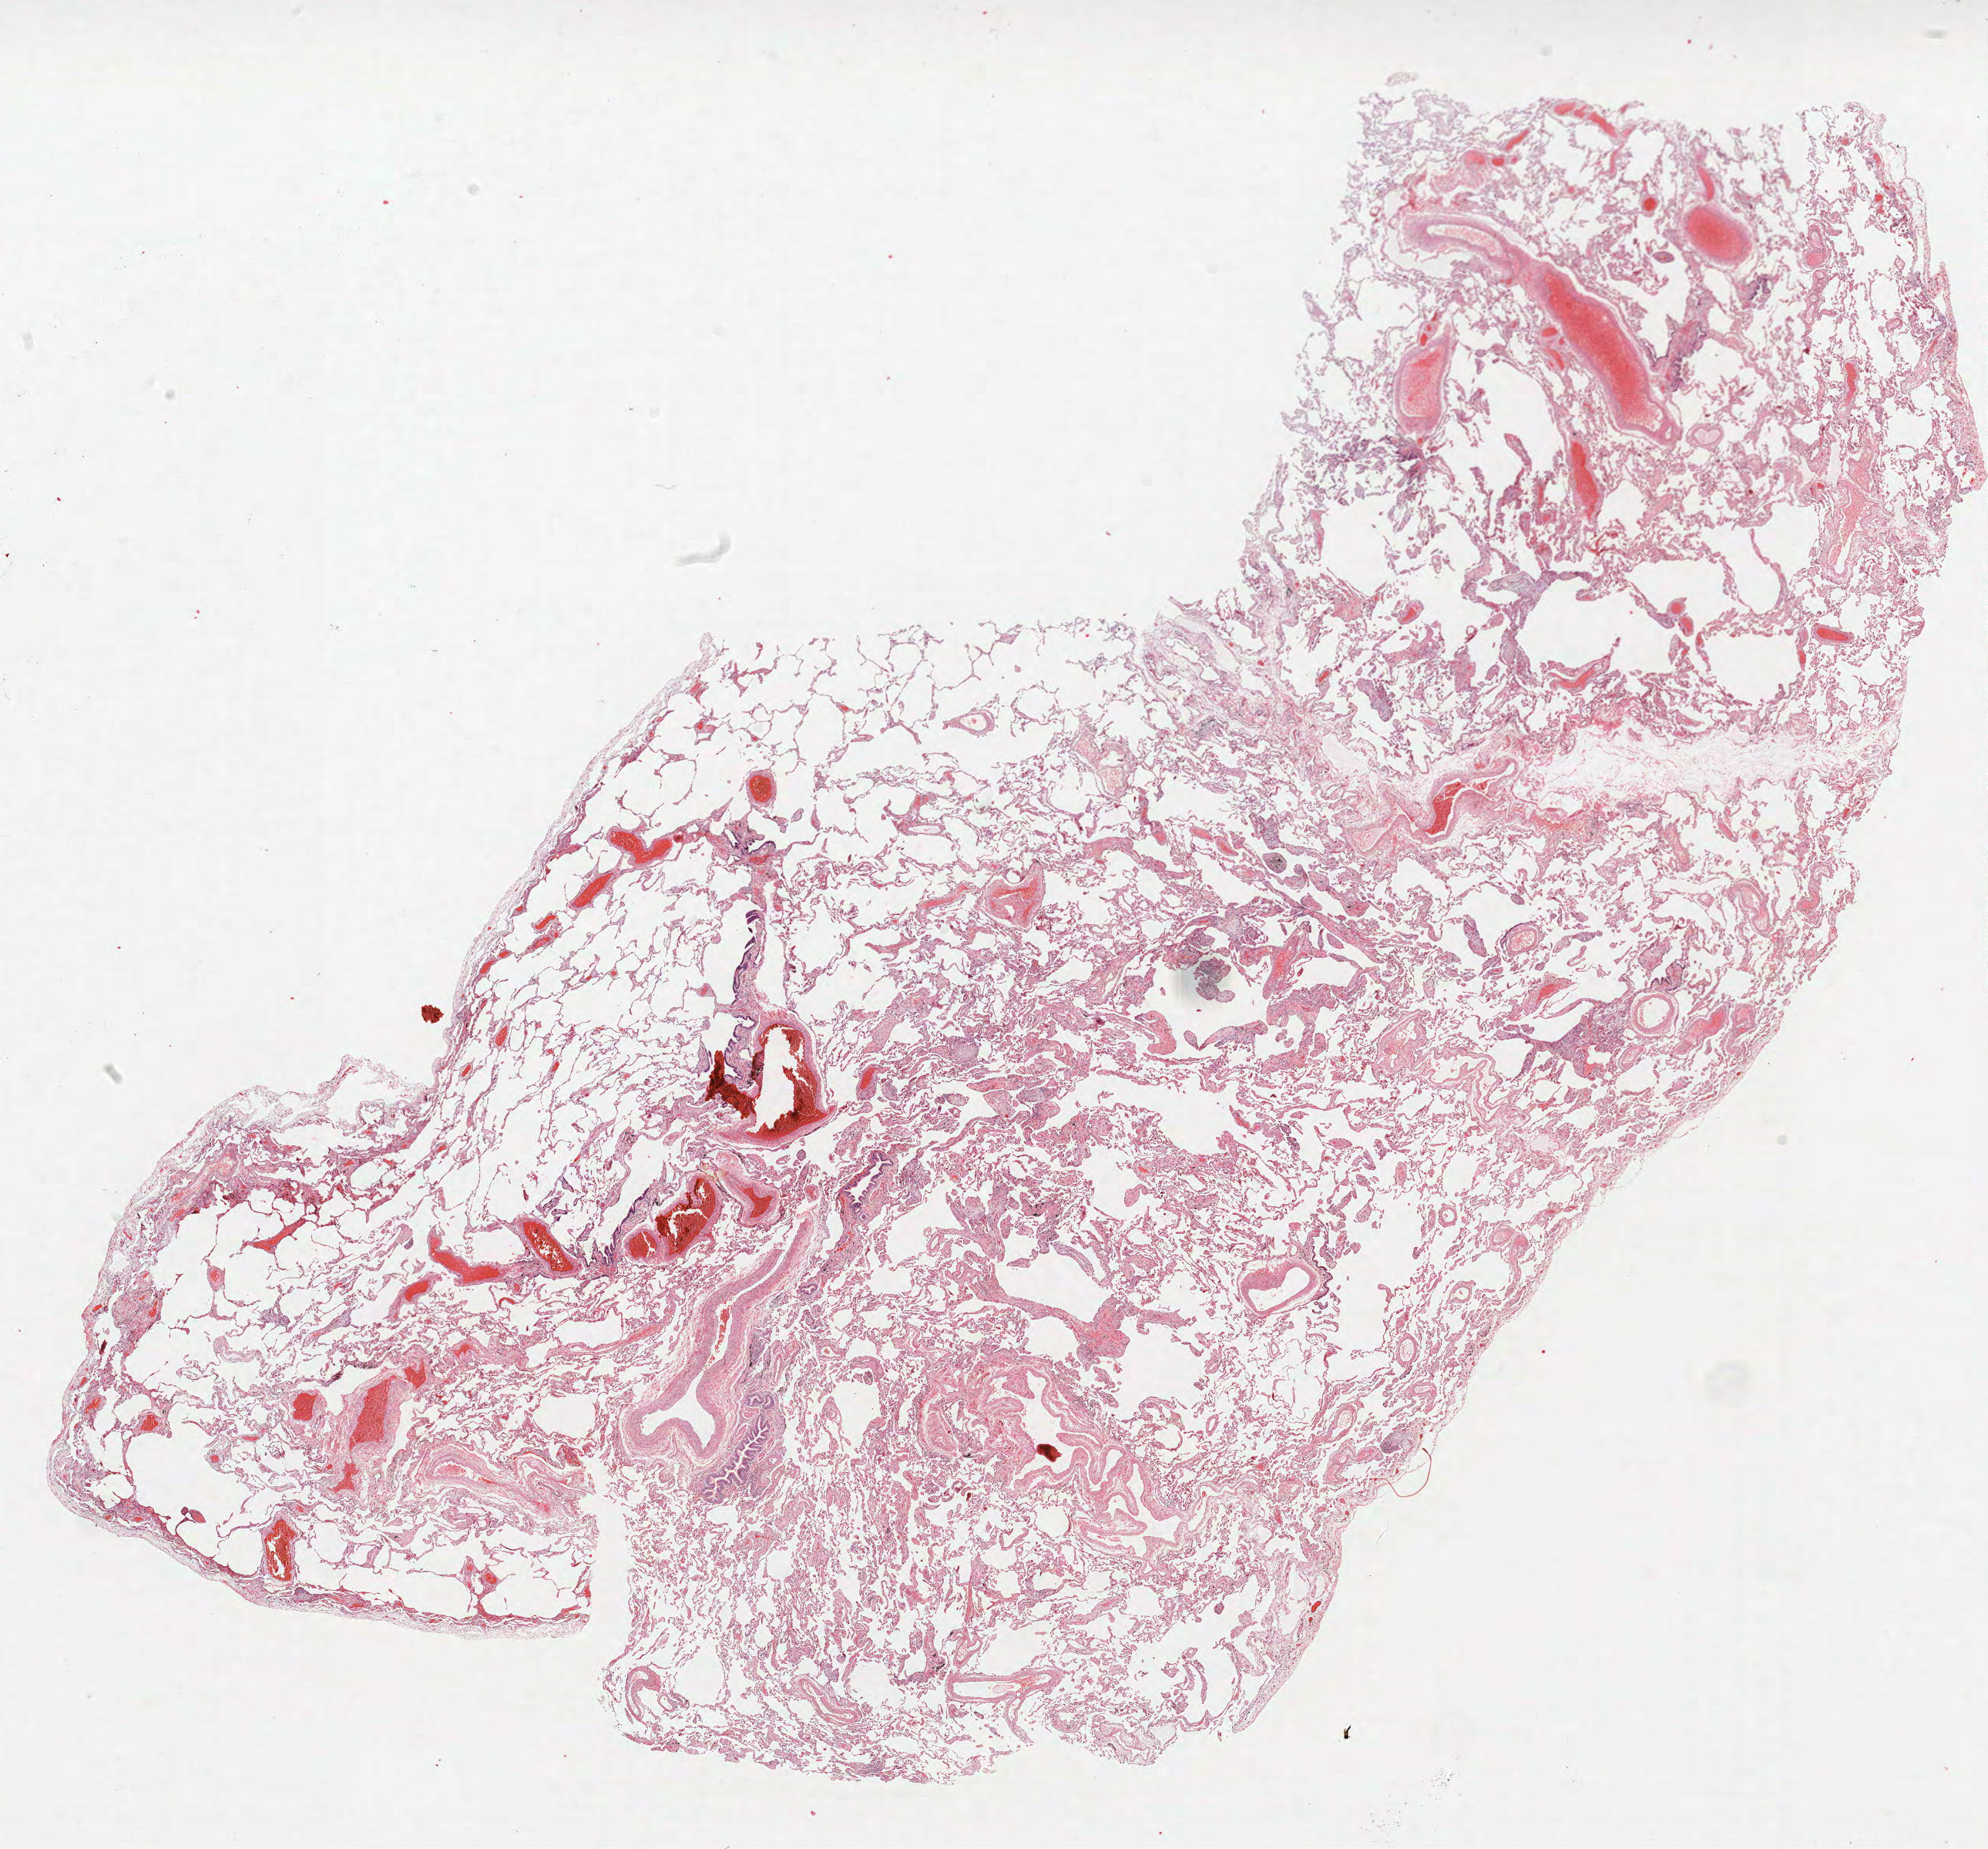
Whole-slide histology image, H&E-stained — a low-resolution overview of the entire scanned area, about 20.6 x 19.2 mm (slide scanned at 40x), formalin-fixed paraffin-embedded (FFPE) section, lung. Male, age 60 at enrolment. Former smoker at enrolment.
Stage (AJCC 6th edition): IA. Primary tumour location (clinical record): right lower lobe. Participant's lung-cancer diagnosis: Neoplasm, malignant (ICD-O-3 8000/3). Tumour size (pathology): 20 mm.